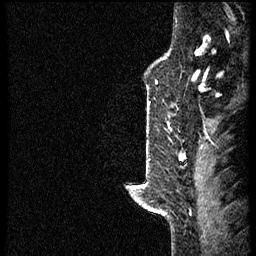
Breast MRI (dynamic contrast-enhanced), one sagittal slice; position 49 of 56 along the scan axis; dynamic contrast-enhanced study with each time point stored as its own series, time point 2 of 3 at this slice position (early post-contrast, ordered by acquisition time); 1.5 T; TE 4.2 ms, TR 21.3 ms; 2 mm slice thickness; 256 × 256 image matrix, field of view 200 × 200 mm. Female patient, age 41 years. From the clinical record (not read from this slice): setting: breast cancer imaged before/during neoadjuvant chemotherapy; receptor status: HER2-positive.
Annotated regions visible in this slice (semi-automatic segmentation, software-assisted and operator-edited):
- analysis volume of interest (the breast-tissue region the enhancement analysis was run in; not a lesion): bounding box <125,73,177,205> (left, top, right, bottom; pixels)
- tumour enhancement mask (voxels above the 100 % enhancement threshold inside the analysis volume of interest): <147,107,171,129>